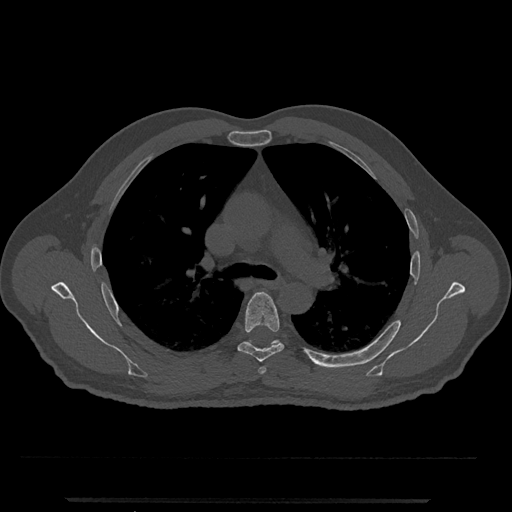
CT including the spine, one axial slice; reconstruction kernel Br40s/3; 120 kVp; bone window (W 1800 / L 400 HU); 0.5 mm slice thickness; 512 × 512 image matrix. Patient: male, 63 years. From the clinical record (not read from this slice): primary cancer: prostate.
Outlined on this slice (semi-automatically segmented with operator editing):
- T5 vertebra: bounding box (x1, y1, x2, y2) in pixels: (238, 292, 284, 362)
- T6 vertebra: (249, 340, 281, 346)